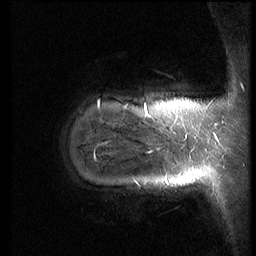
Breast MRI (dynamic contrast-enhanced), one sagittal slice. Slice 14 of 66 in the series (ordered by position). Dynamic contrast-enhanced series, image 2 of 3 at this slice position (ordered by acquisition). 1.5 T. TE 4.2 ms, TR 8.9 ms. 2.5 mm slice thickness. 256 × 256 image matrix, field of view 200 × 200 mm. Patient: female, 39 years. Case-level facts recorded for this patient, not image findings: setting: breast cancer imaged before/during neoadjuvant chemotherapy; receptor status: HER2-positive.
Outlined on this slice (semi-automatically segmented with operator editing):
- analysis volume of interest (the breast-tissue region the enhancement analysis was run in; not a lesion): box from (x=58, y=75) to (x=188, y=218) px
- tumour enhancement mask (voxels above the 140 % enhancement threshold inside the analysis volume of interest): (x=95, y=101)–(x=147, y=160)